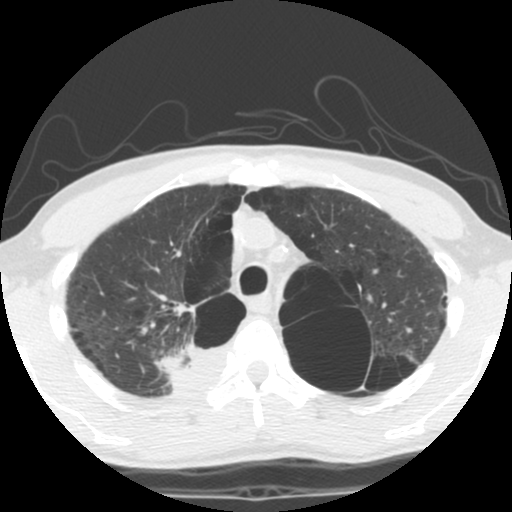
Chest CT (low-dose screening protocol), one axial image. Second screening round (one year after baseline). Lung window (W 1500 / L -600 HU). 2.5 mm slice thickness. 512 × 512 image matrix. Male, age 62 years at enrolment. Current smoker at enrolment.
Expert-annotated lung lesion, box from (x=127, y=324) to (x=222, y=400) px. The exam's reader record, not a measurement of the box and not confirmed to be the same lesion: non-calcified nodule or mass ≥4 mm, 35 × 25 mm, soft tissue attenuation. Official screen result: positive, other. Lung cancer was diagnosed 14 days after this screen: non-small cell carcinoma, right upper lobe, poorly differentiated (G3), stage IA (AJCC 6th edition), 70 mm at pathology.